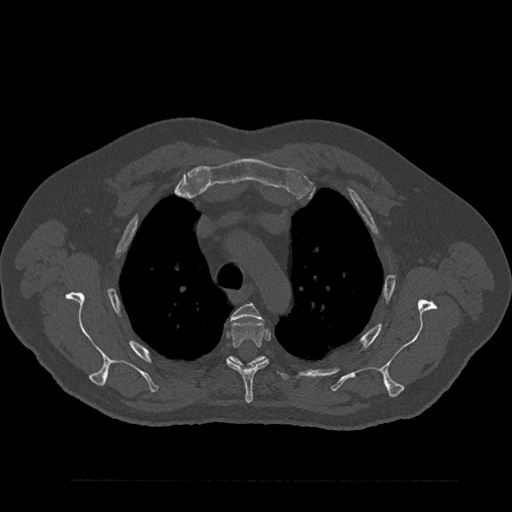
CT including the spine, one axial slice. Slice 640 of 797 in the series (ordered by position). Reconstruction kernel Br40s/3. 120 kVp. Bone window (W 1800 / L 400 HU). 512 × 512 image matrix, field of view 430 × 430 mm. Patient: male, 61 years. From the clinical record (not read from this slice): primary cancer: prostate.
Outlined on this slice (semi-automatic segmentation, software-assisted and operator-edited):
- T3 vertebra: bounding box <231,303,262,320> (left, top, right, bottom; pixels)
- T4 vertebra: <226,321,269,403>
- T5 vertebra: <229,356,290,380>